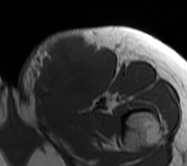
MRI of an extremity soft-tissue mass, one axial slice; position 23 of 62 along the scan axis; MR volume resampled by the dataset authors to the PET/CT grid (not the native acquisition matrix); 3.27 mm slice thickness; 187 × 166 image matrix, field of view 183 × 162 mm. Female patient. From the clinical record (not read from this slice): histological type: leiomyosarcoma; grade: high; site of the primary tumour: groin.
Annotated regions visible in this slice (expert contour drawn on MRI and transferred to this co-registered scan by the dataset authors):
- gross tumour volume including surrounding oedema: bounding box [x1, y1, x2, y2] px = [18, 26, 117, 109]
- gross tumour volume (mass): [39, 33, 115, 105]